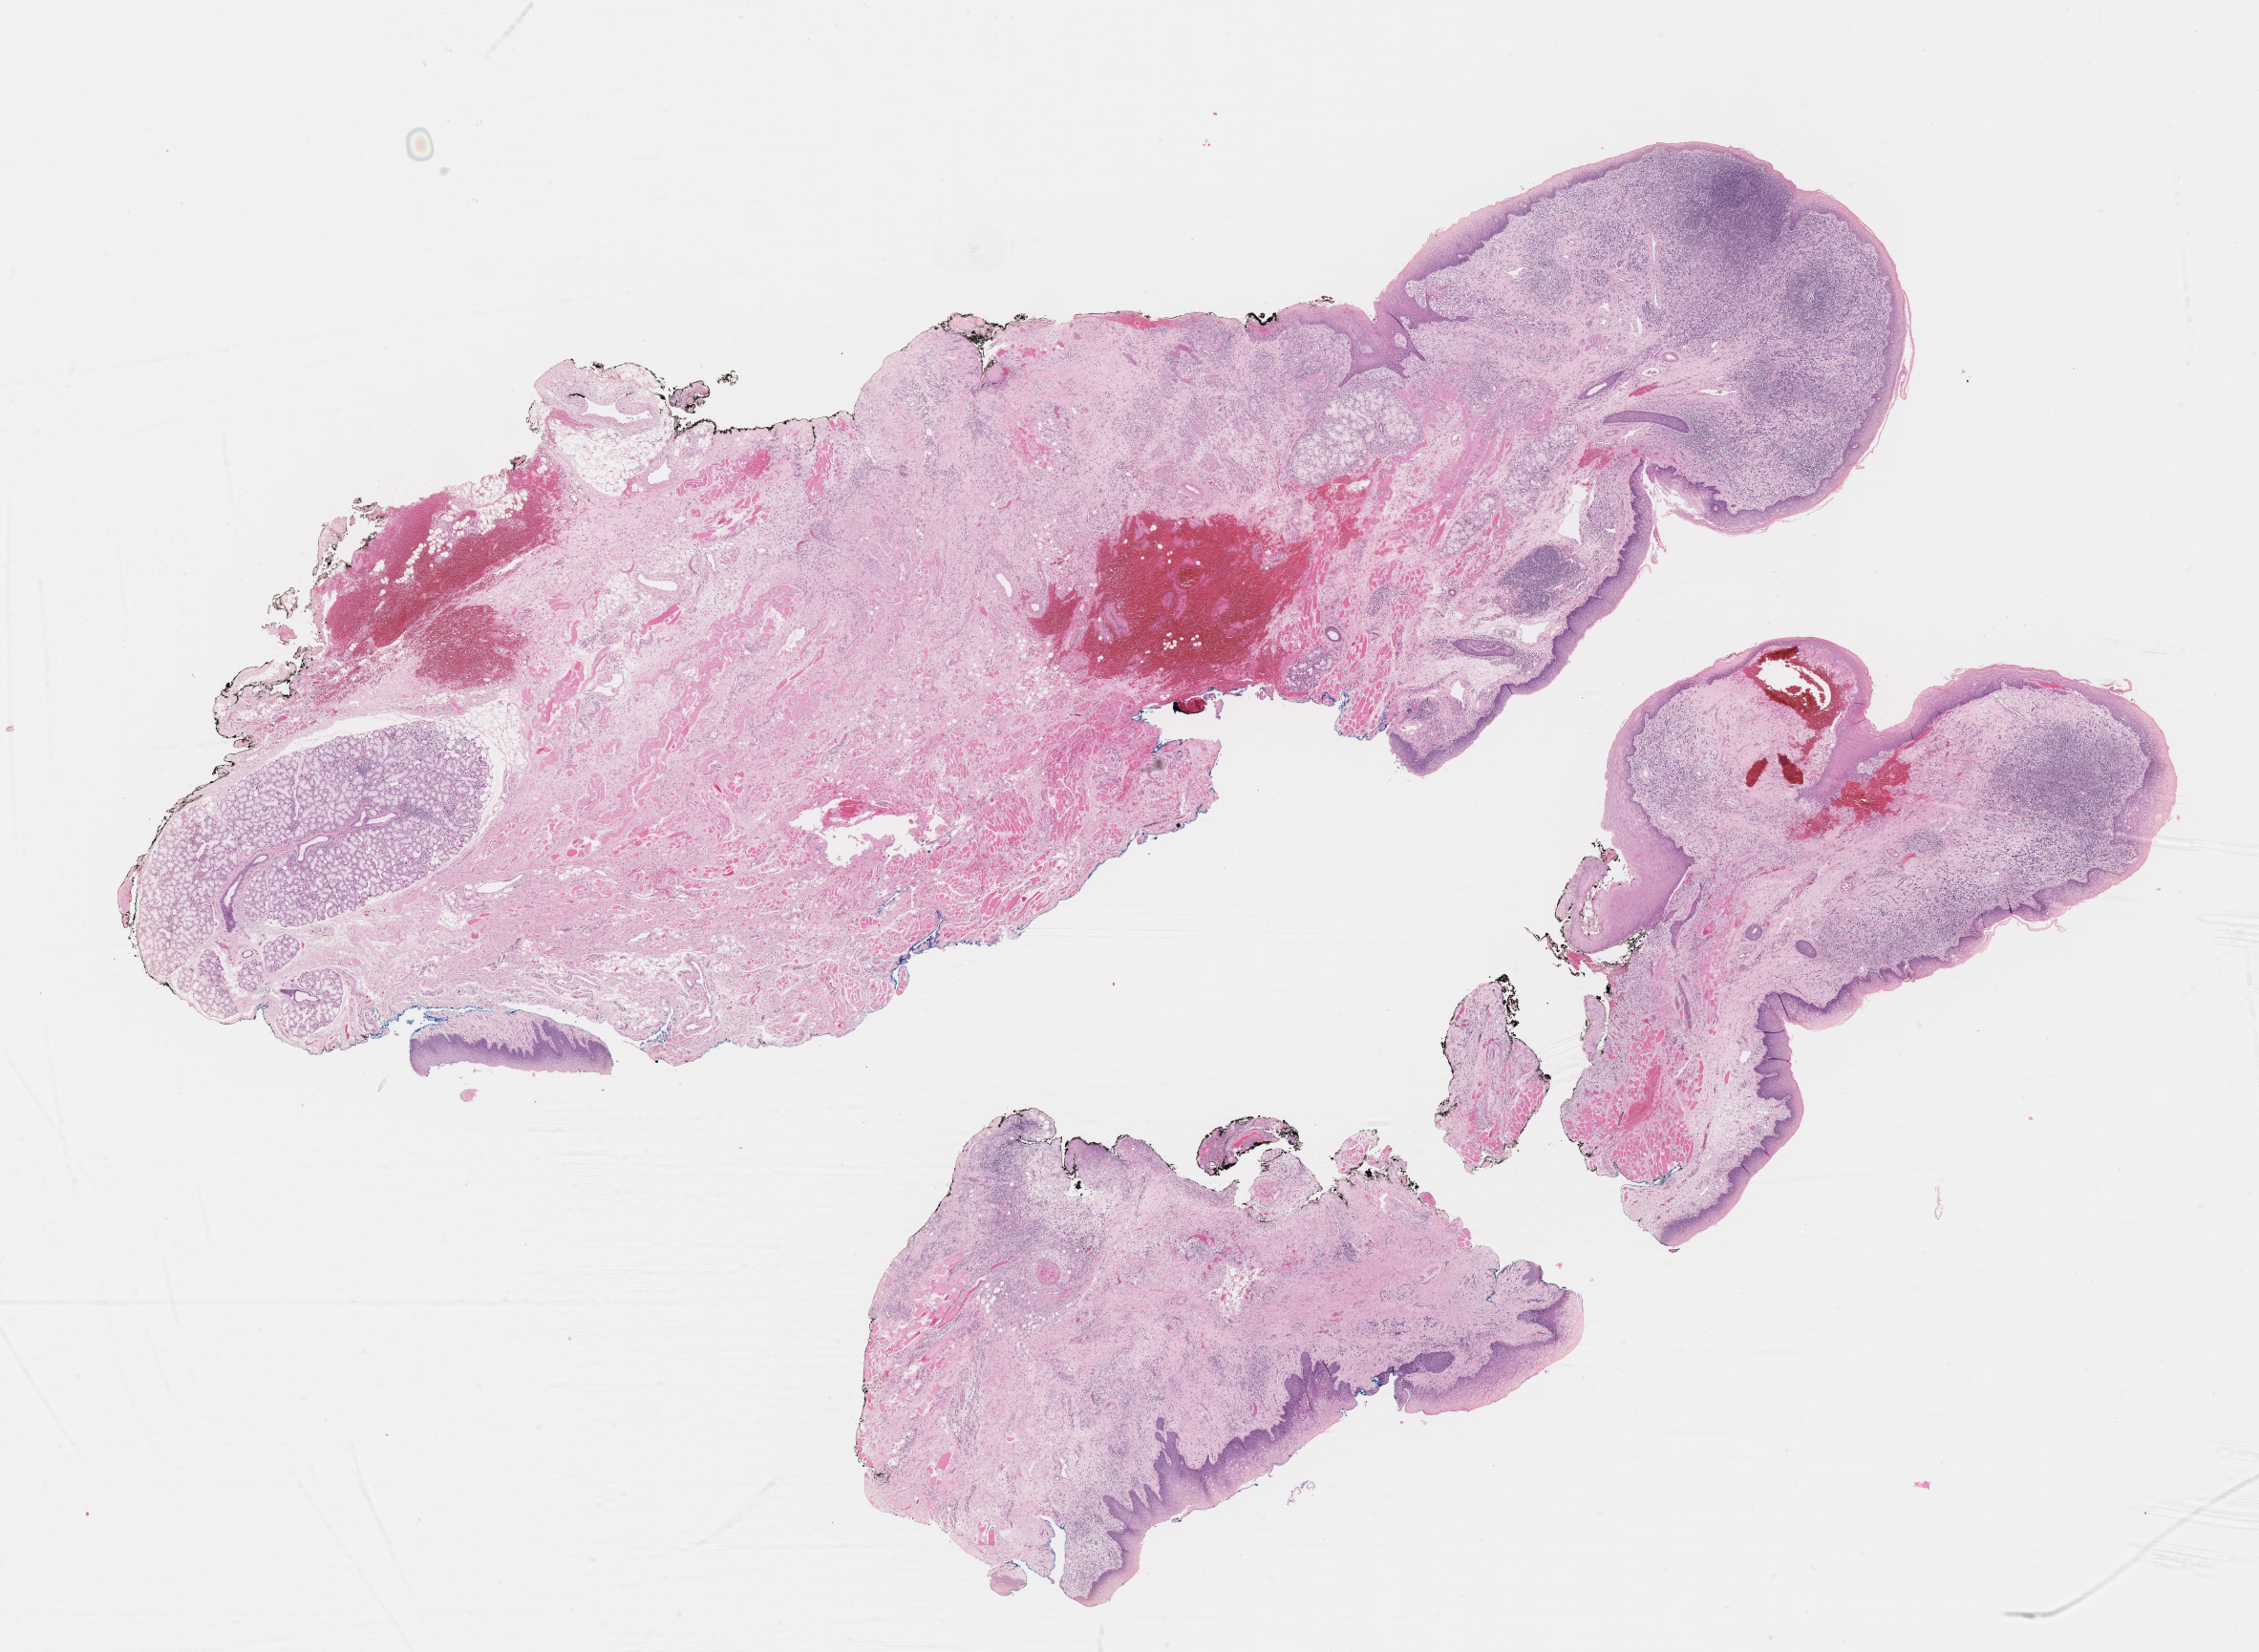
Digitized H&E-stained section of tumor tissue, low-resolution overview of the scanned area, about 19.1 x 14.0 mm, FFPE section. Male patient, age at diagnosis 12.0 years.
Diagnosis: rhabdomyosarcoma; histological classification: embryonal rhabdomyosarcoma.